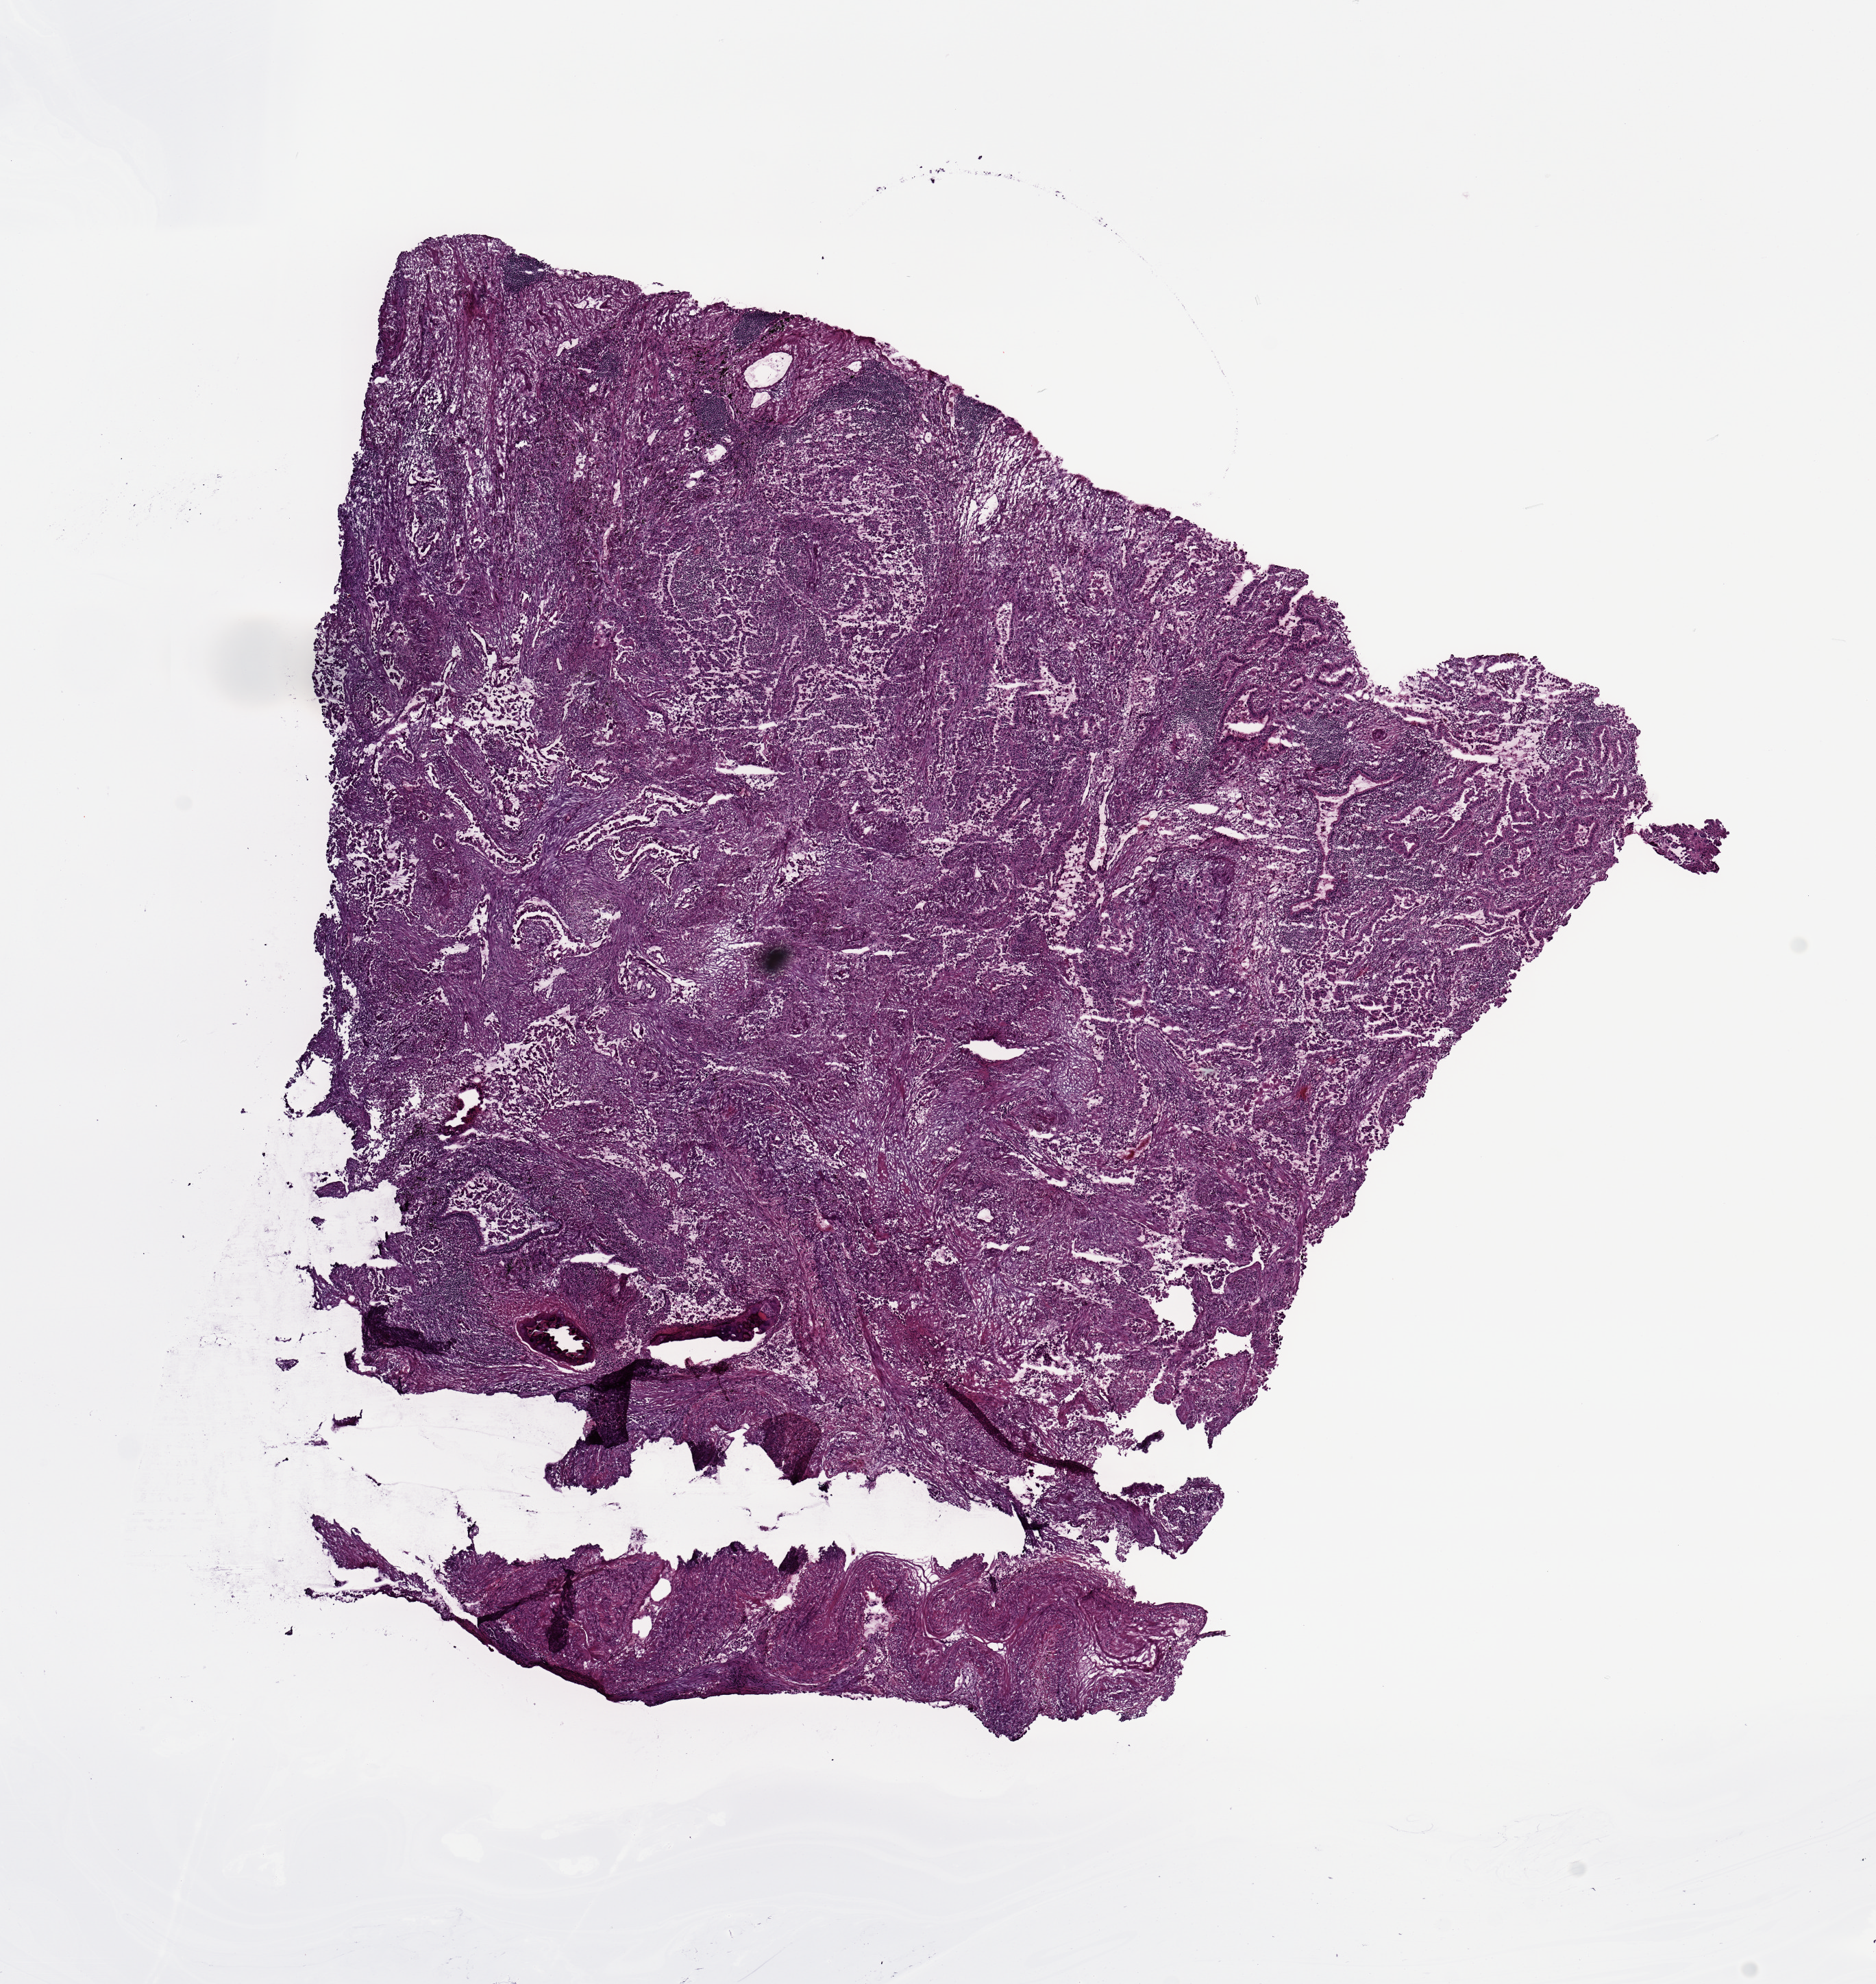
Digitized H&E tissue section (whole slide), low-resolution overview of the scanned area, about 10.8 x 11.5 mm. Lung, tumour tissue. 72-year-old female patient. Histologic grade: G2 (moderately differentiated).
Primary tumour site (as recorded): left upper lobe. Histologic diagnosis: Adenocarcinoma, NOS. AJCC pathologic stage: IB.